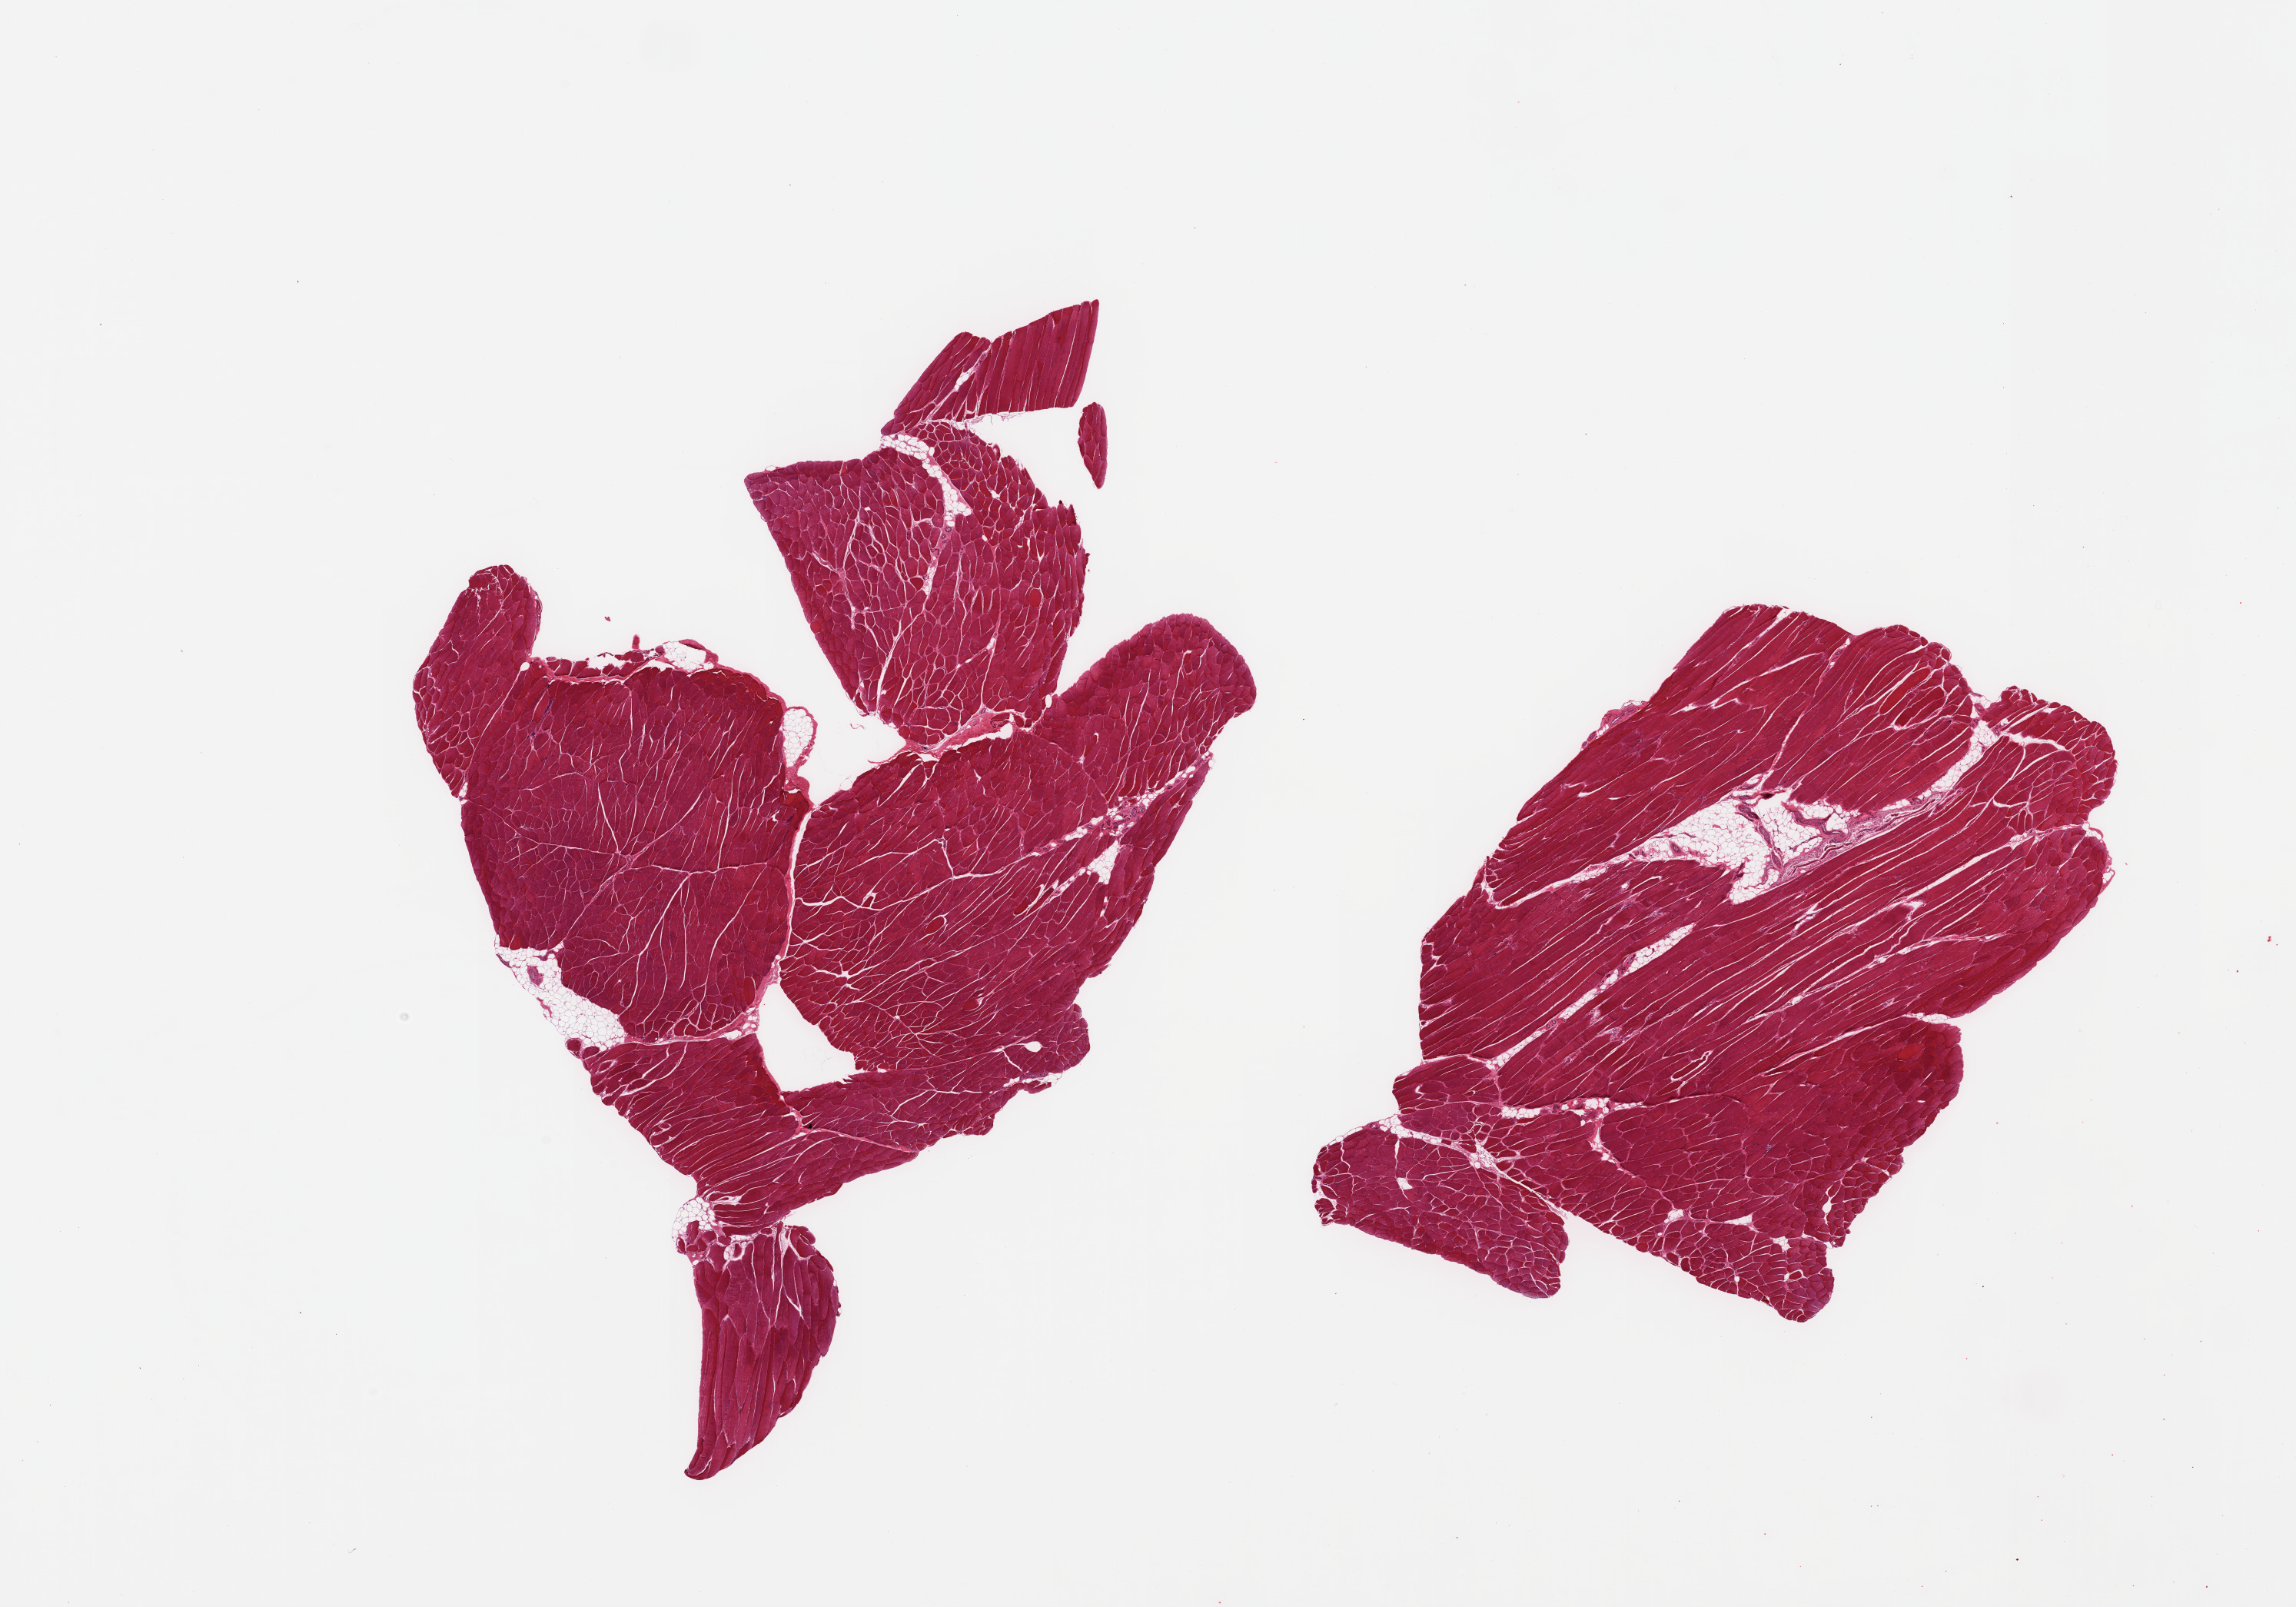
Digitized haematoxylin and eosin-stained section, brightfield, low-resolution overview of the scanned area, about 23.6 x 16.5 mm. PAXgene-fixed paraffin-embedded (PFPE) section. Sampled site (target tissue): skeletal muscle. Donor tissue sample.
Review note (as recorded): 2 pieces; 5% internal fat.